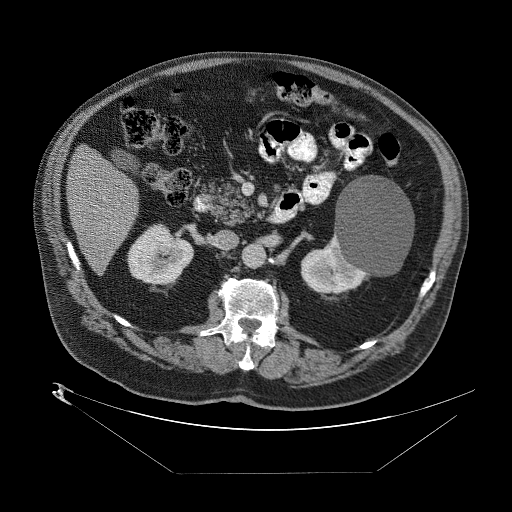
Contrast-enhanced abdominal CT (liver protocol), one axial slice; slice 22 of 89 in the series (ordered by position); reconstruction kernel STANDARD; 140 kVp; one of 2 acquisitions stored at this slice position; soft-tissue window (W 400 / L 40 HU); 512 × 512 image matrix. Case-level facts recorded for this patient, not image findings: diagnosis: hepatocellular carcinoma (patient treated with transarterial chemoembolisation; whether this scan precedes or follows treatment is not stated here); TNM stage (as recorded): Stage-II; Child-Pugh class: B; tumour size: 4 cm.
Structures marked on this image (semi-automatically segmented with operator editing):
- abdominal aorta: bounding box (x1, y1, x2, y2) in pixels: (243, 244, 265, 267)
- liver parenchyma outside the tumour (the mass and vessels are separate outlines, so this box may not span the whole liver): (64, 141, 138, 270)
- liver vessels: (98, 197, 110, 237)